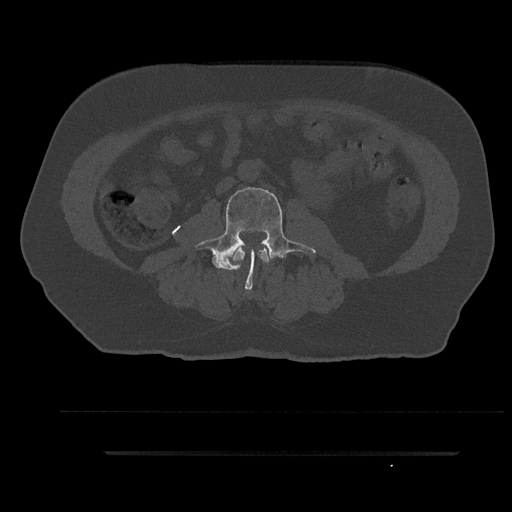
CT including the spine, one axial slice. Position 51 of 797 along the scan axis. Reconstruction kernel Br40s/3. 120 kVp. Bone window (W 1800 / L 400 HU). 0.5 mm slice thickness. 512 × 512 image matrix, field of view 432 × 432 mm. Patient: male, 63 years. From the clinical record (not read from this slice): primary cancer: renal.
Outlined on this slice (semi-automatically segmented with operator editing):
- L2 vertebra: box from (x=232, y=248) to (x=269, y=270) px
- L3 vertebra: (x=194, y=185)–(x=316, y=289)